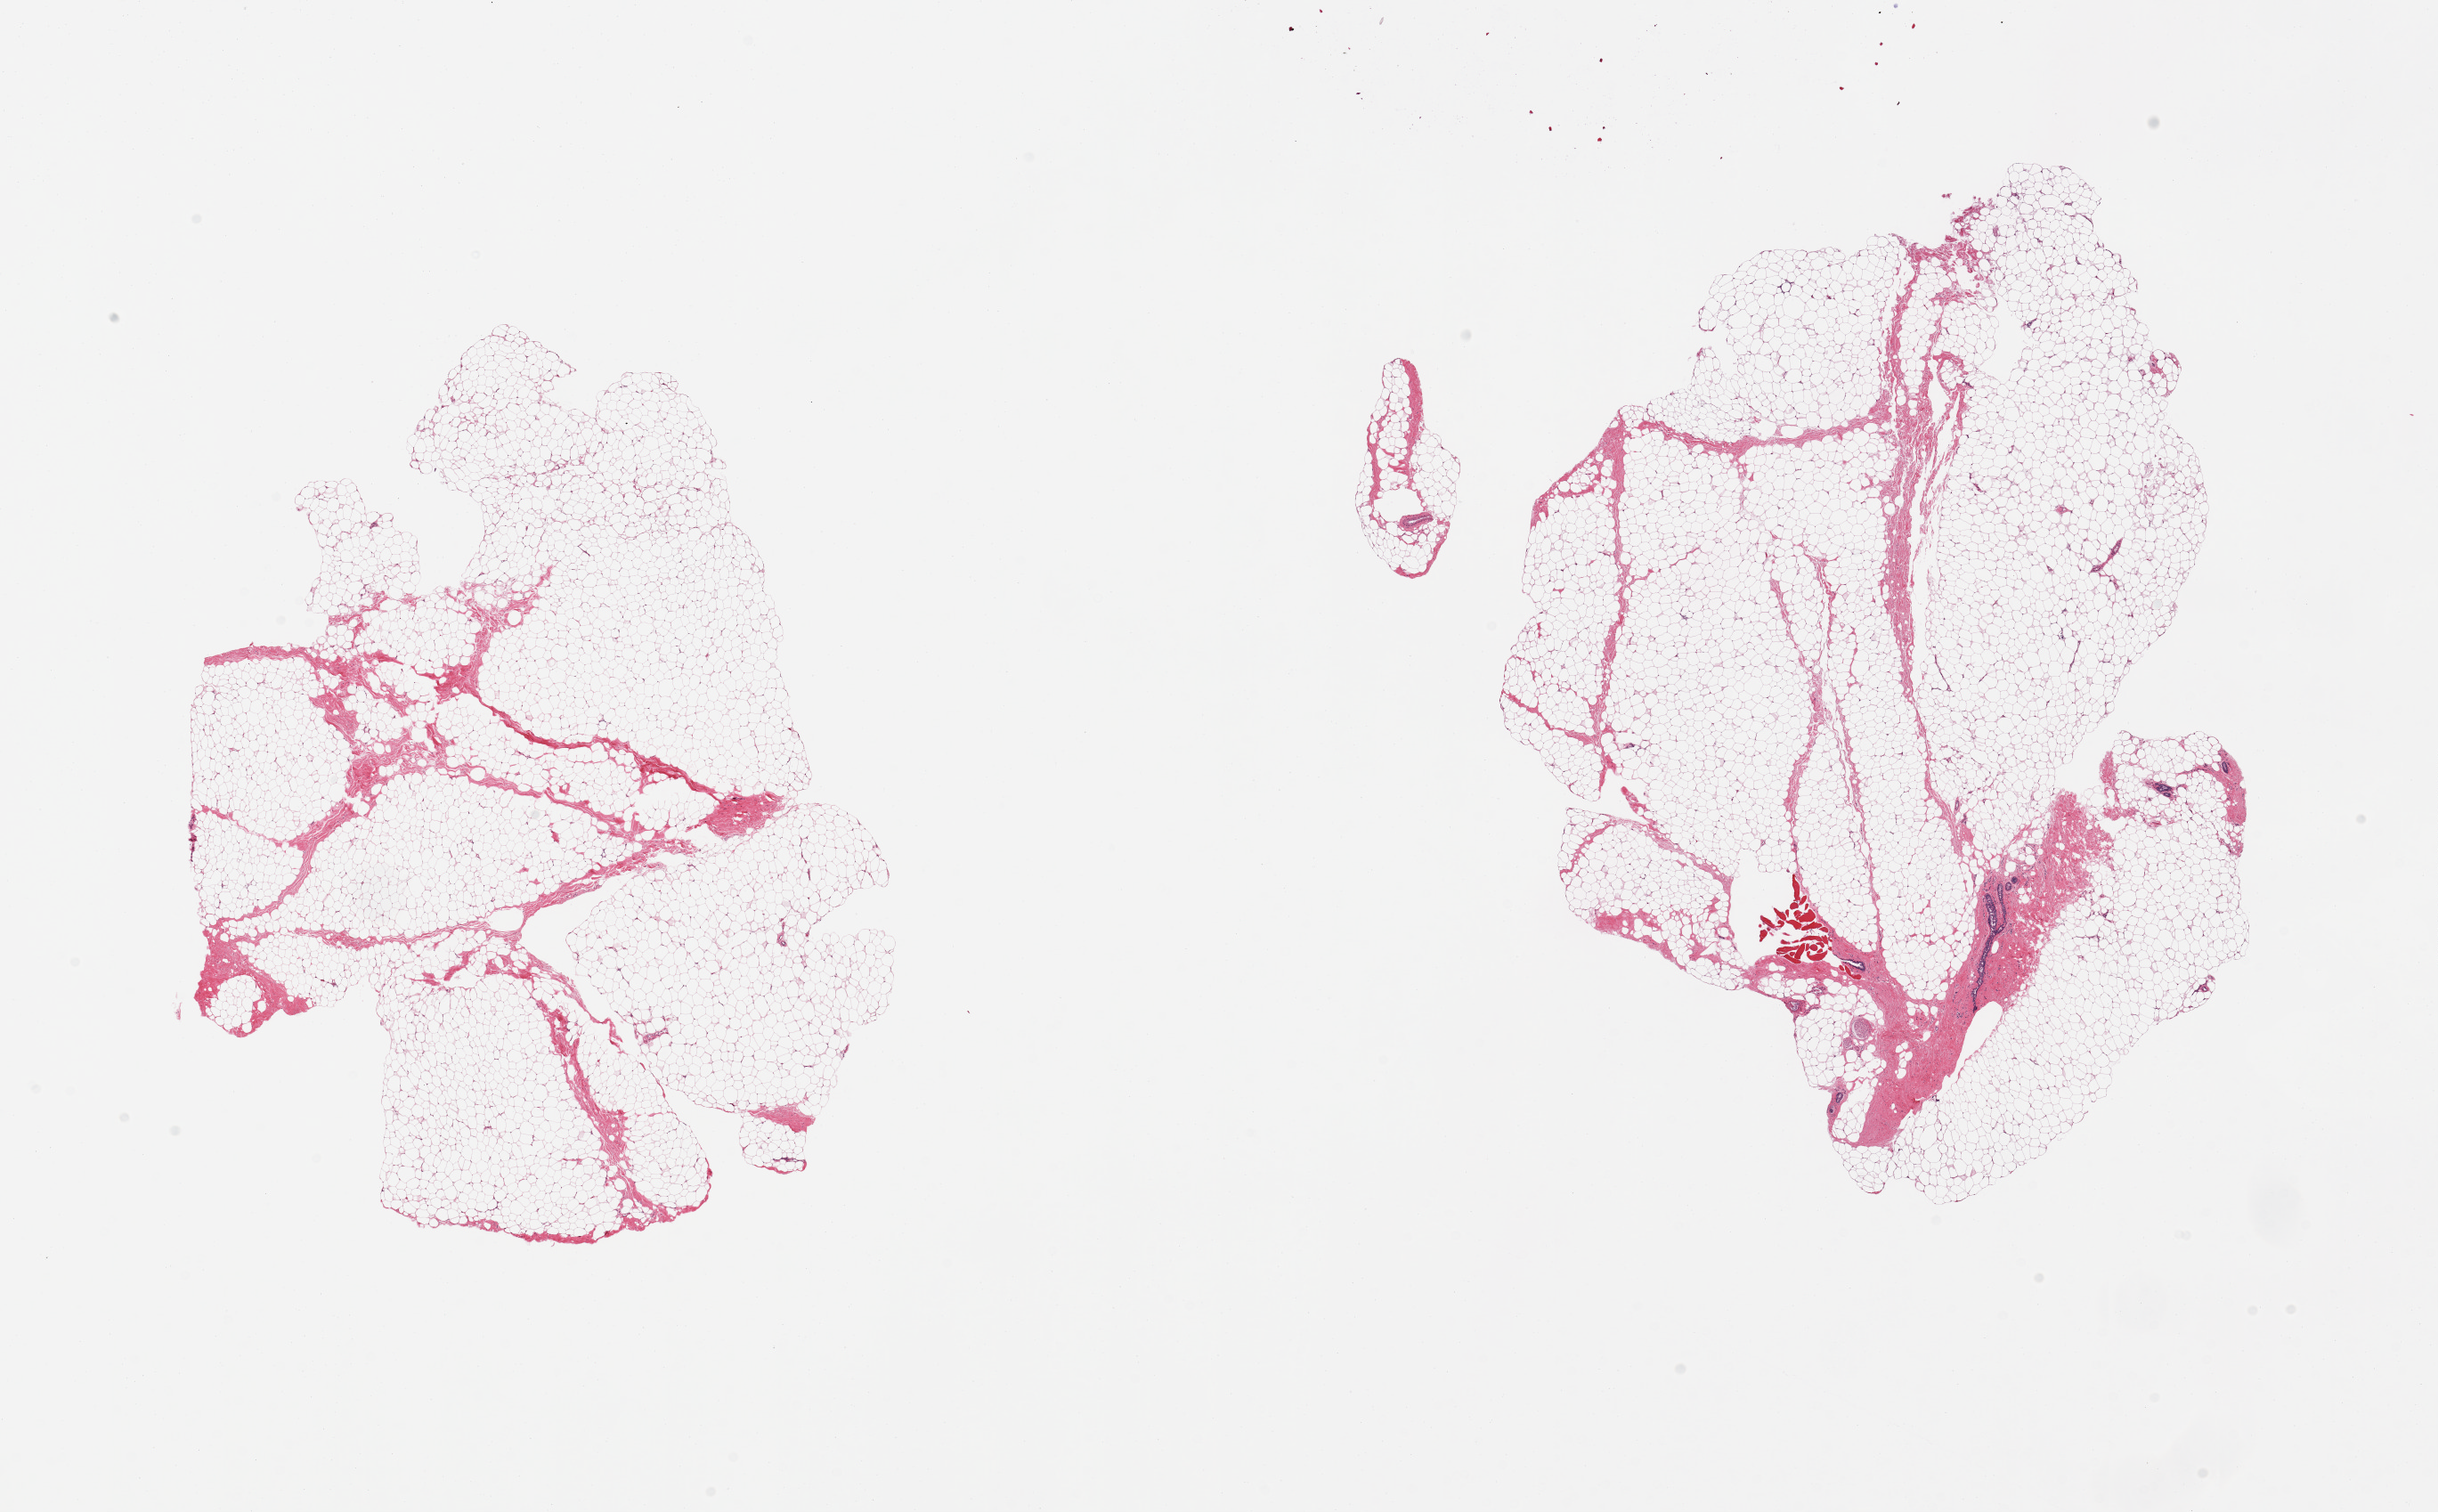
Haematoxylin and eosin whole-slide image, shown as a low-resolution overview of the whole scanned area (about 21.7 x 13.4 mm), PAXgene-fixed paraffin-embedded (PFPE) section, sampled site (target tissue): breast, donor tissue sample. Donor: male.
Reviewer comment on this tissue sample: 2 pieces, mainly fibroadipose, gynecomastoid hyerplasia, milde; trace ductal elements; peripheral nerve; skeletal muscle fibres (all rep).